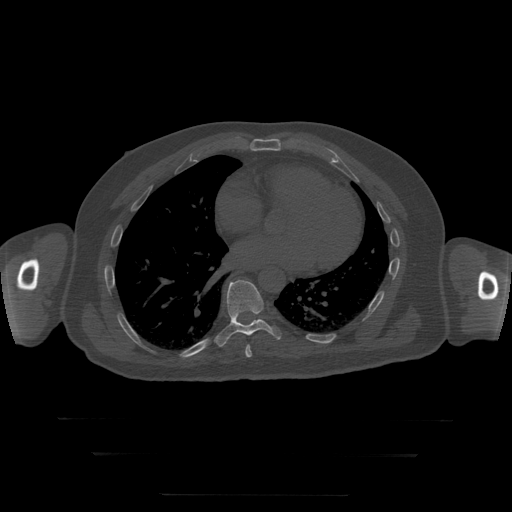
CT including the spine, one axial slice; slice 146 of 397 in the series (ordered by position); reconstruction kernel STANDARD; 120 kVp; bone window (W 1800 / L 400 HU); 512 × 512 image matrix, field of view 510 × 510 mm. Patient age 73 years. From the clinical record (not read from this slice): primary cancer: prostate.
Annotated regions visible in this slice (semi-automatic segmentation, software-assisted and operator-edited):
- T8 vertebra: bounding box [x1, y1, x2, y2] px = [245, 345, 252, 358]
- T9 vertebra: [215, 280, 282, 347]